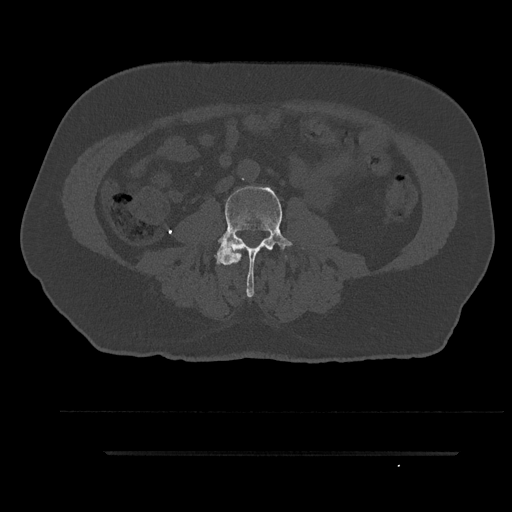
CT including the spine, one axial slice. Reconstruction kernel Br40s/3. 120 kVp. Bone window (W 1800 / L 400 HU). 0.5 mm slice thickness. 512 × 512 image matrix, field of view 432 × 432 mm. Patient: male, 63 years. Case-level facts recorded for this patient, not image findings: primary cancer: renal; vertebrae with lytic lesions (as recorded): T8.
Annotated regions visible in this slice (semi-automatic segmentation, software-assisted and operator-edited):
- L2 vertebra: bounding box <239,255,242,259> (left, top, right, bottom; pixels)
- L3 vertebra: <214,185,306,298>